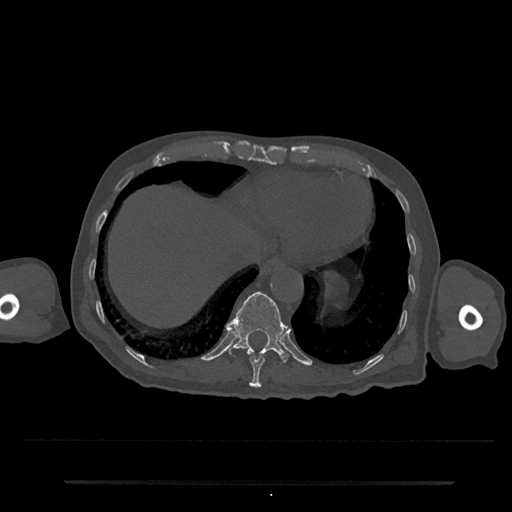
CT including the spine, one axial slice; slice 277 of 797 in the series (ordered by position); 120 kVp; bone window (W 1800 / L 400 HU); 0.5 mm slice thickness; 512 × 512 image matrix. Patient: male, 74 years. Case-level facts recorded for this patient, not image findings: primary cancer: prostate.
Structures marked on this image (semi-automatic segmentation, software-assisted and operator-edited):
- T10 vertebra: bounding box [x1, y1, x2, y2] px = [249, 355, 265, 388]
- T11 vertebra: [227, 292, 289, 362]